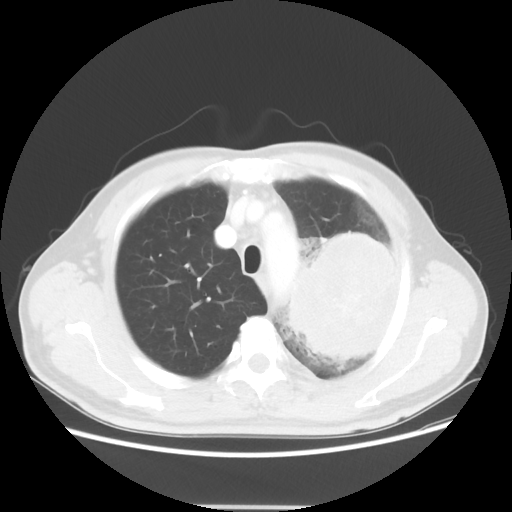
Chest CT, one axial slice; slice 43 of 53 in the series (ordered by position); reconstruction kernel STANDARD; 100 kVp; lung window (W 1500 / L -600 HU); 5 mm slice thickness; 512 × 512 image matrix. Patient: male, 60 years. Case-level facts recorded for this patient, not image findings: clinical TNM (as recorded): T4 N1 M1a; histopathological grade: G3.
Structures marked on this image (bounding box drawn by a radiologist):
- lung tumour (recorded histology: large cell carcinoma): bounding box <281,230,401,367> (left, top, right, bottom; pixels)